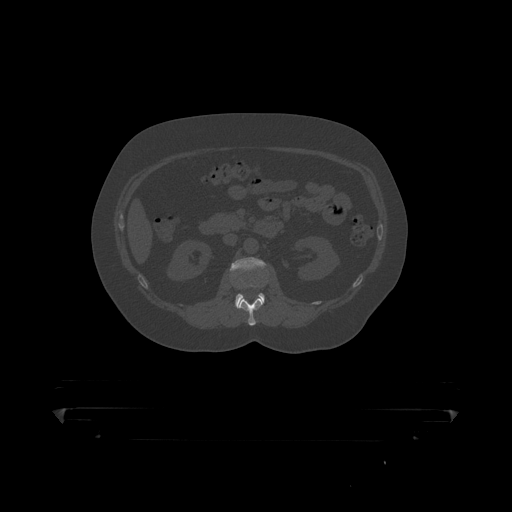
CT including the spine, one axial slice. Position 132 of 390 along the scan axis. 120 kVp. Bone window (W 1800 / L 400 HU). 1.25 mm slice thickness. 512 × 512 image matrix, field of view 650 × 650 mm. Male patient, age 60 years. Case-level facts recorded for this patient, not image findings: primary cancer: prostate.
Outlined on this slice (semi-automatically segmented with operator editing):
- L1 vertebra: bounding box [x1, y1, x2, y2] px = [237, 281, 268, 319]
- L2 vertebra: [231, 257, 266, 309]